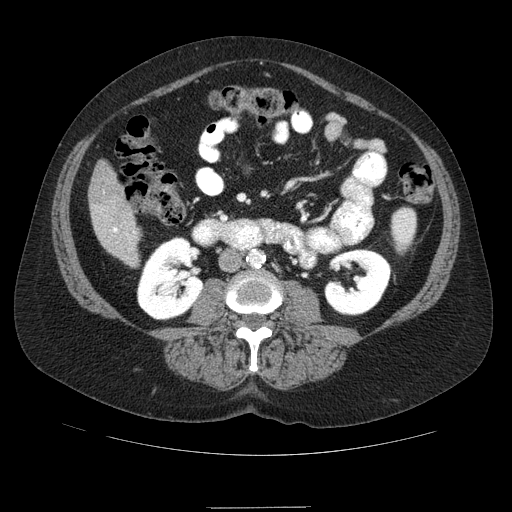
Contrast-enhanced abdominal CT (liver protocol), one axial slice; position 18 of 89 along the scan axis; reconstruction kernel STANDARD; soft-tissue window (W 400 / L 40 HU); 512 × 512 image matrix, field of view 400 × 400 mm. From the clinical record (not read from this slice): diagnosis: hepatocellular carcinoma (patient treated with transarterial chemoembolisation; whether this scan precedes or follows treatment is not stated here); TNM stage (as recorded): Stage-IIIB; Child-Pugh class: A; tumour nodularity: multinodular.
Annotated regions visible in this slice (semi-automatically segmented with operator editing):
- liver parenchyma outside the tumour (the mass and vessels are separate outlines, so this box may not span the whole liver): bounding box [x1, y1, x2, y2] px = [88, 160, 140, 262]
- liver vessels: [112, 227, 135, 233]